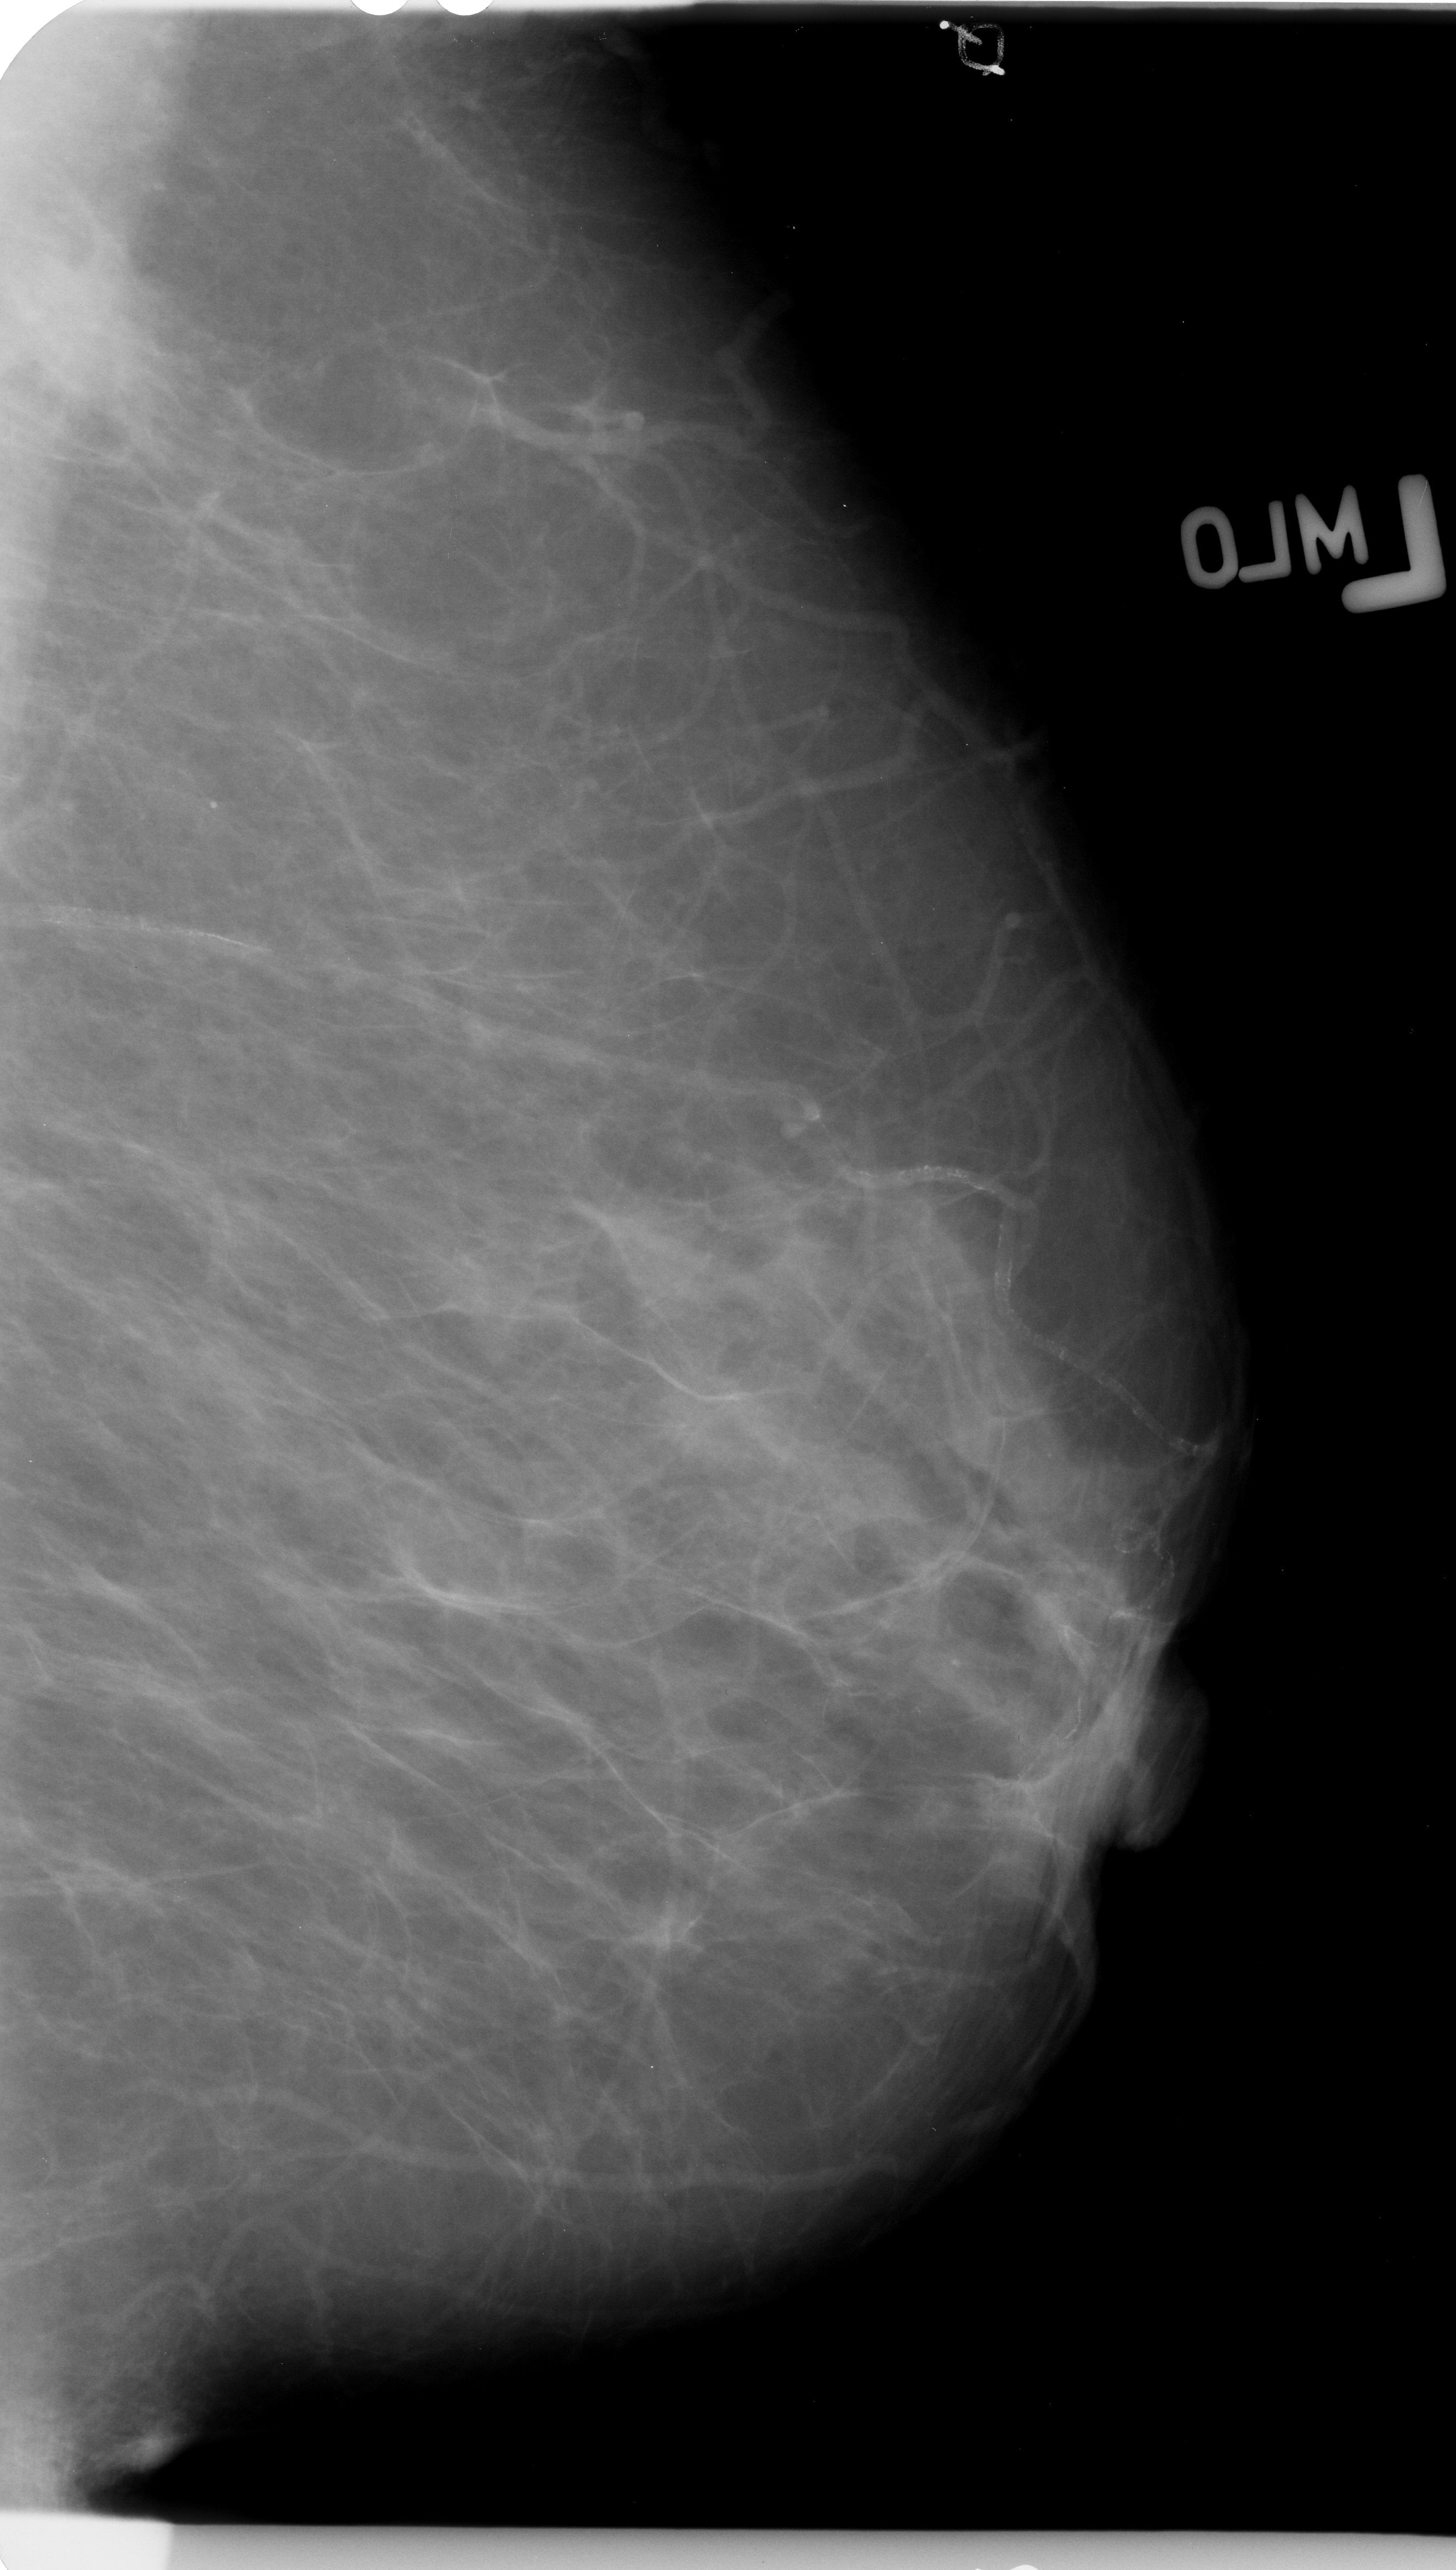
Digitized screen-film mammogram, left breast, mediolateral oblique (MLO) view, breast composition: scattered fibroglandular densities (BI-RADS density category 2 of 4).
Abnormality record for this image: mass, shape irregular, margins spiculated; BI-RADS assessment category 4; subtlety rating 4 on a 1 (subtle) to 5 (obvious) scale; pathology (as recorded): malignant.